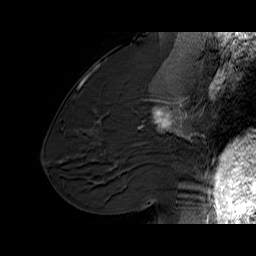
Breast MRI (dynamic contrast-enhanced), one sagittal slice. Position 32 of 60 along the scan axis. Dynamic contrast-enhanced series, time point 2 of 6 at this slice position (early post-contrast). 1.5 T. TE 6.1 ms, TR 32.9 ms. 4 mm slice thickness. 256 × 256 image matrix, field of view 220 × 220 mm. Female patient. Case-level facts recorded for this patient, not image findings: setting: breast cancer imaged before/during neoadjuvant chemotherapy; receptor status: HER2-positive.
Outlined on this slice (semi-automatically segmented with operator editing):
- analysis volume of interest (the breast-tissue region the enhancement analysis was run in; not a lesion): bounding box [x1, y1, x2, y2] px = [127, 95, 194, 165]
- tumour enhancement mask (voxels above the 100 % enhancement threshold inside the analysis volume of interest): [140, 99, 190, 139]